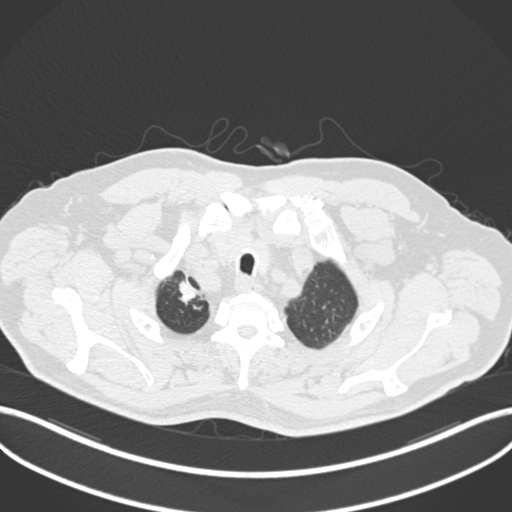
Chest CT, one axial slice. Reconstruction kernel B30f. 120 kVp. Lung window (W 1500 / L -600 HU). 1 mm slice thickness. 512 × 512 image matrix. Patient: male, 60 years. From the clinical record (not read from this slice): clinical TNM (as recorded): T1b N1 M0.
Structures marked on this image (bounding box drawn by a radiologist):
- lung tumour (recorded histology: squamous cell carcinoma): bounding box <169,275,206,314> (left, top, right, bottom; pixels)